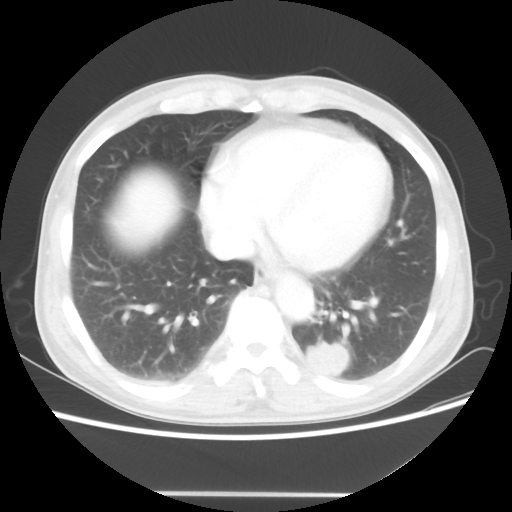
Chest CT, one axial slice. Position 20 of 60 along the scan axis. Reconstruction kernel STANDARD. 100 kVp. Lung window (W 1500 / L -600 HU). 512 × 512 image matrix, field of view 360 × 360 mm. Patient: male, 55 years. From the clinical record (not read from this slice): clinical TNM (as recorded): T1c N3 M0; histopathological grade: G3.
Annotated regions visible in this slice (rectangle marked by the reading radiologist):
- lung tumour (recorded histology: small cell carcinoma): bounding box <301,338,357,377> (left, top, right, bottom; pixels)